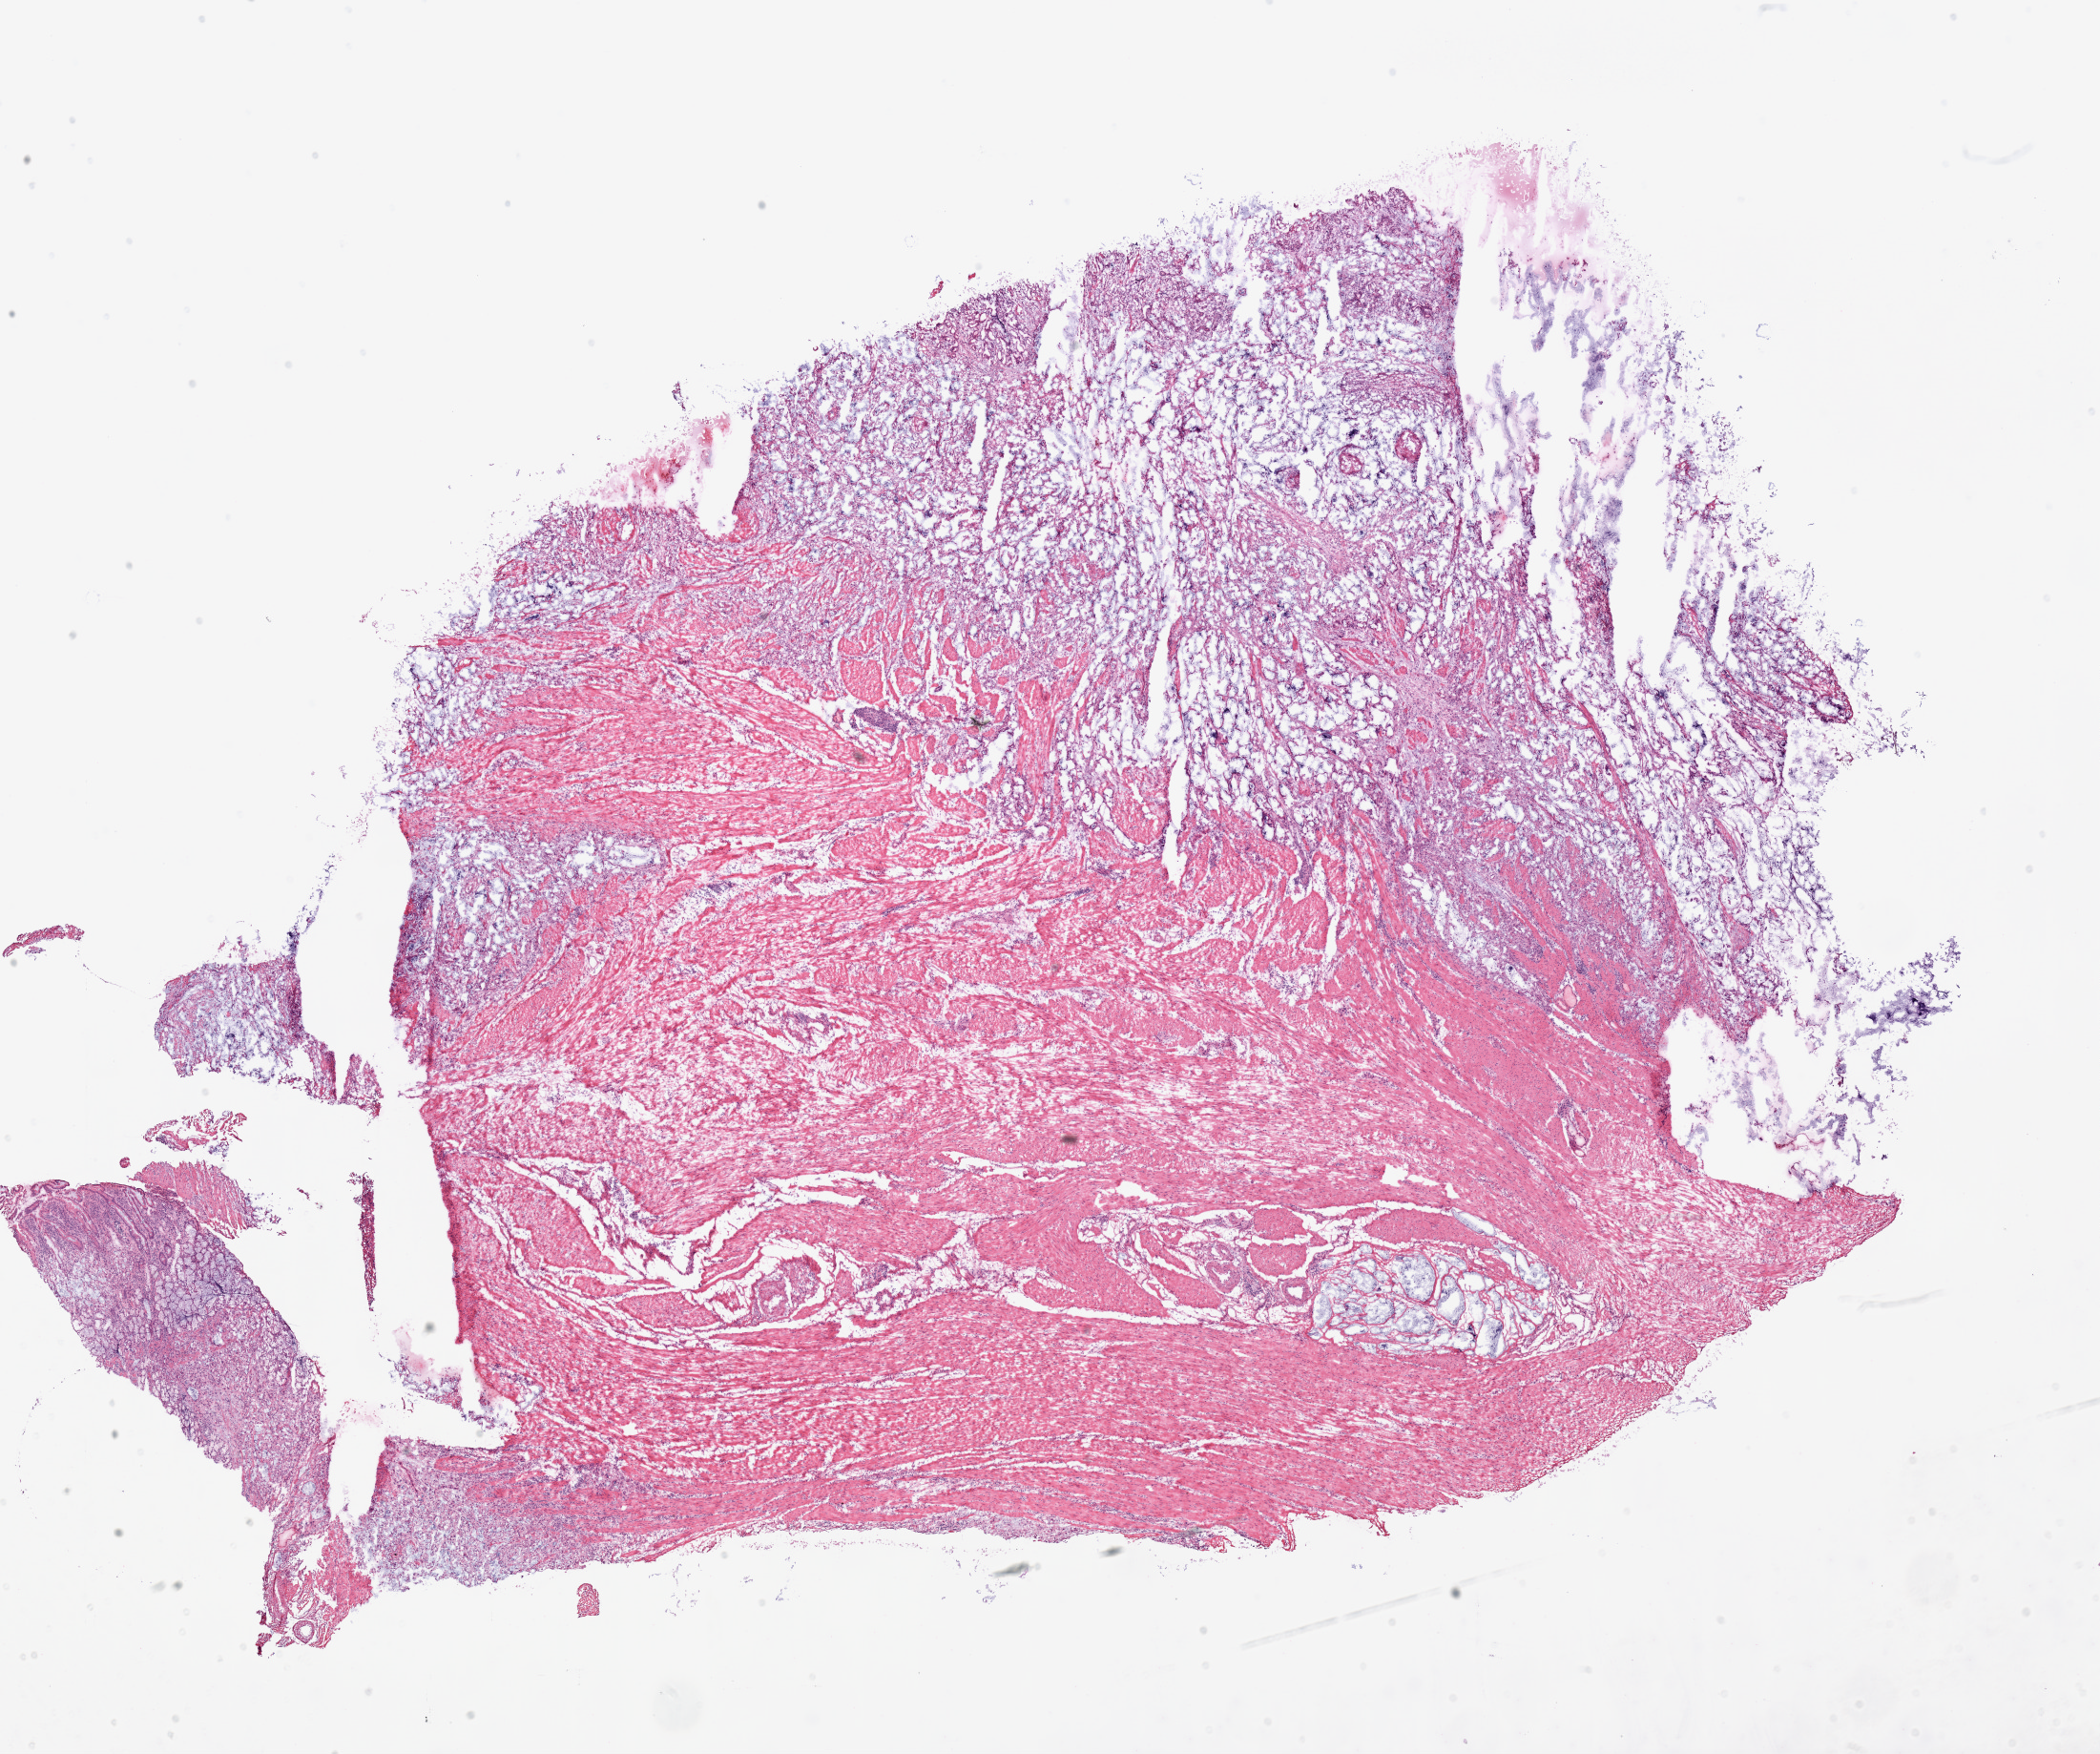
Whole-slide histology image, H&E-stained — a low-resolution overview of the entire scanned area, about 17.5 x 14.6 mm (slide scanned at 20x), frozen section from the top of the tissue portion, primary tumour sample from the stomach. Patient: male, age at initial diagnosis 82 years. Composition of this section per pathologist review: tumour cells 35%, tumour nuclei 75%.
Diagnosis: Mucinous adenocarcinoma (gastric antrum).